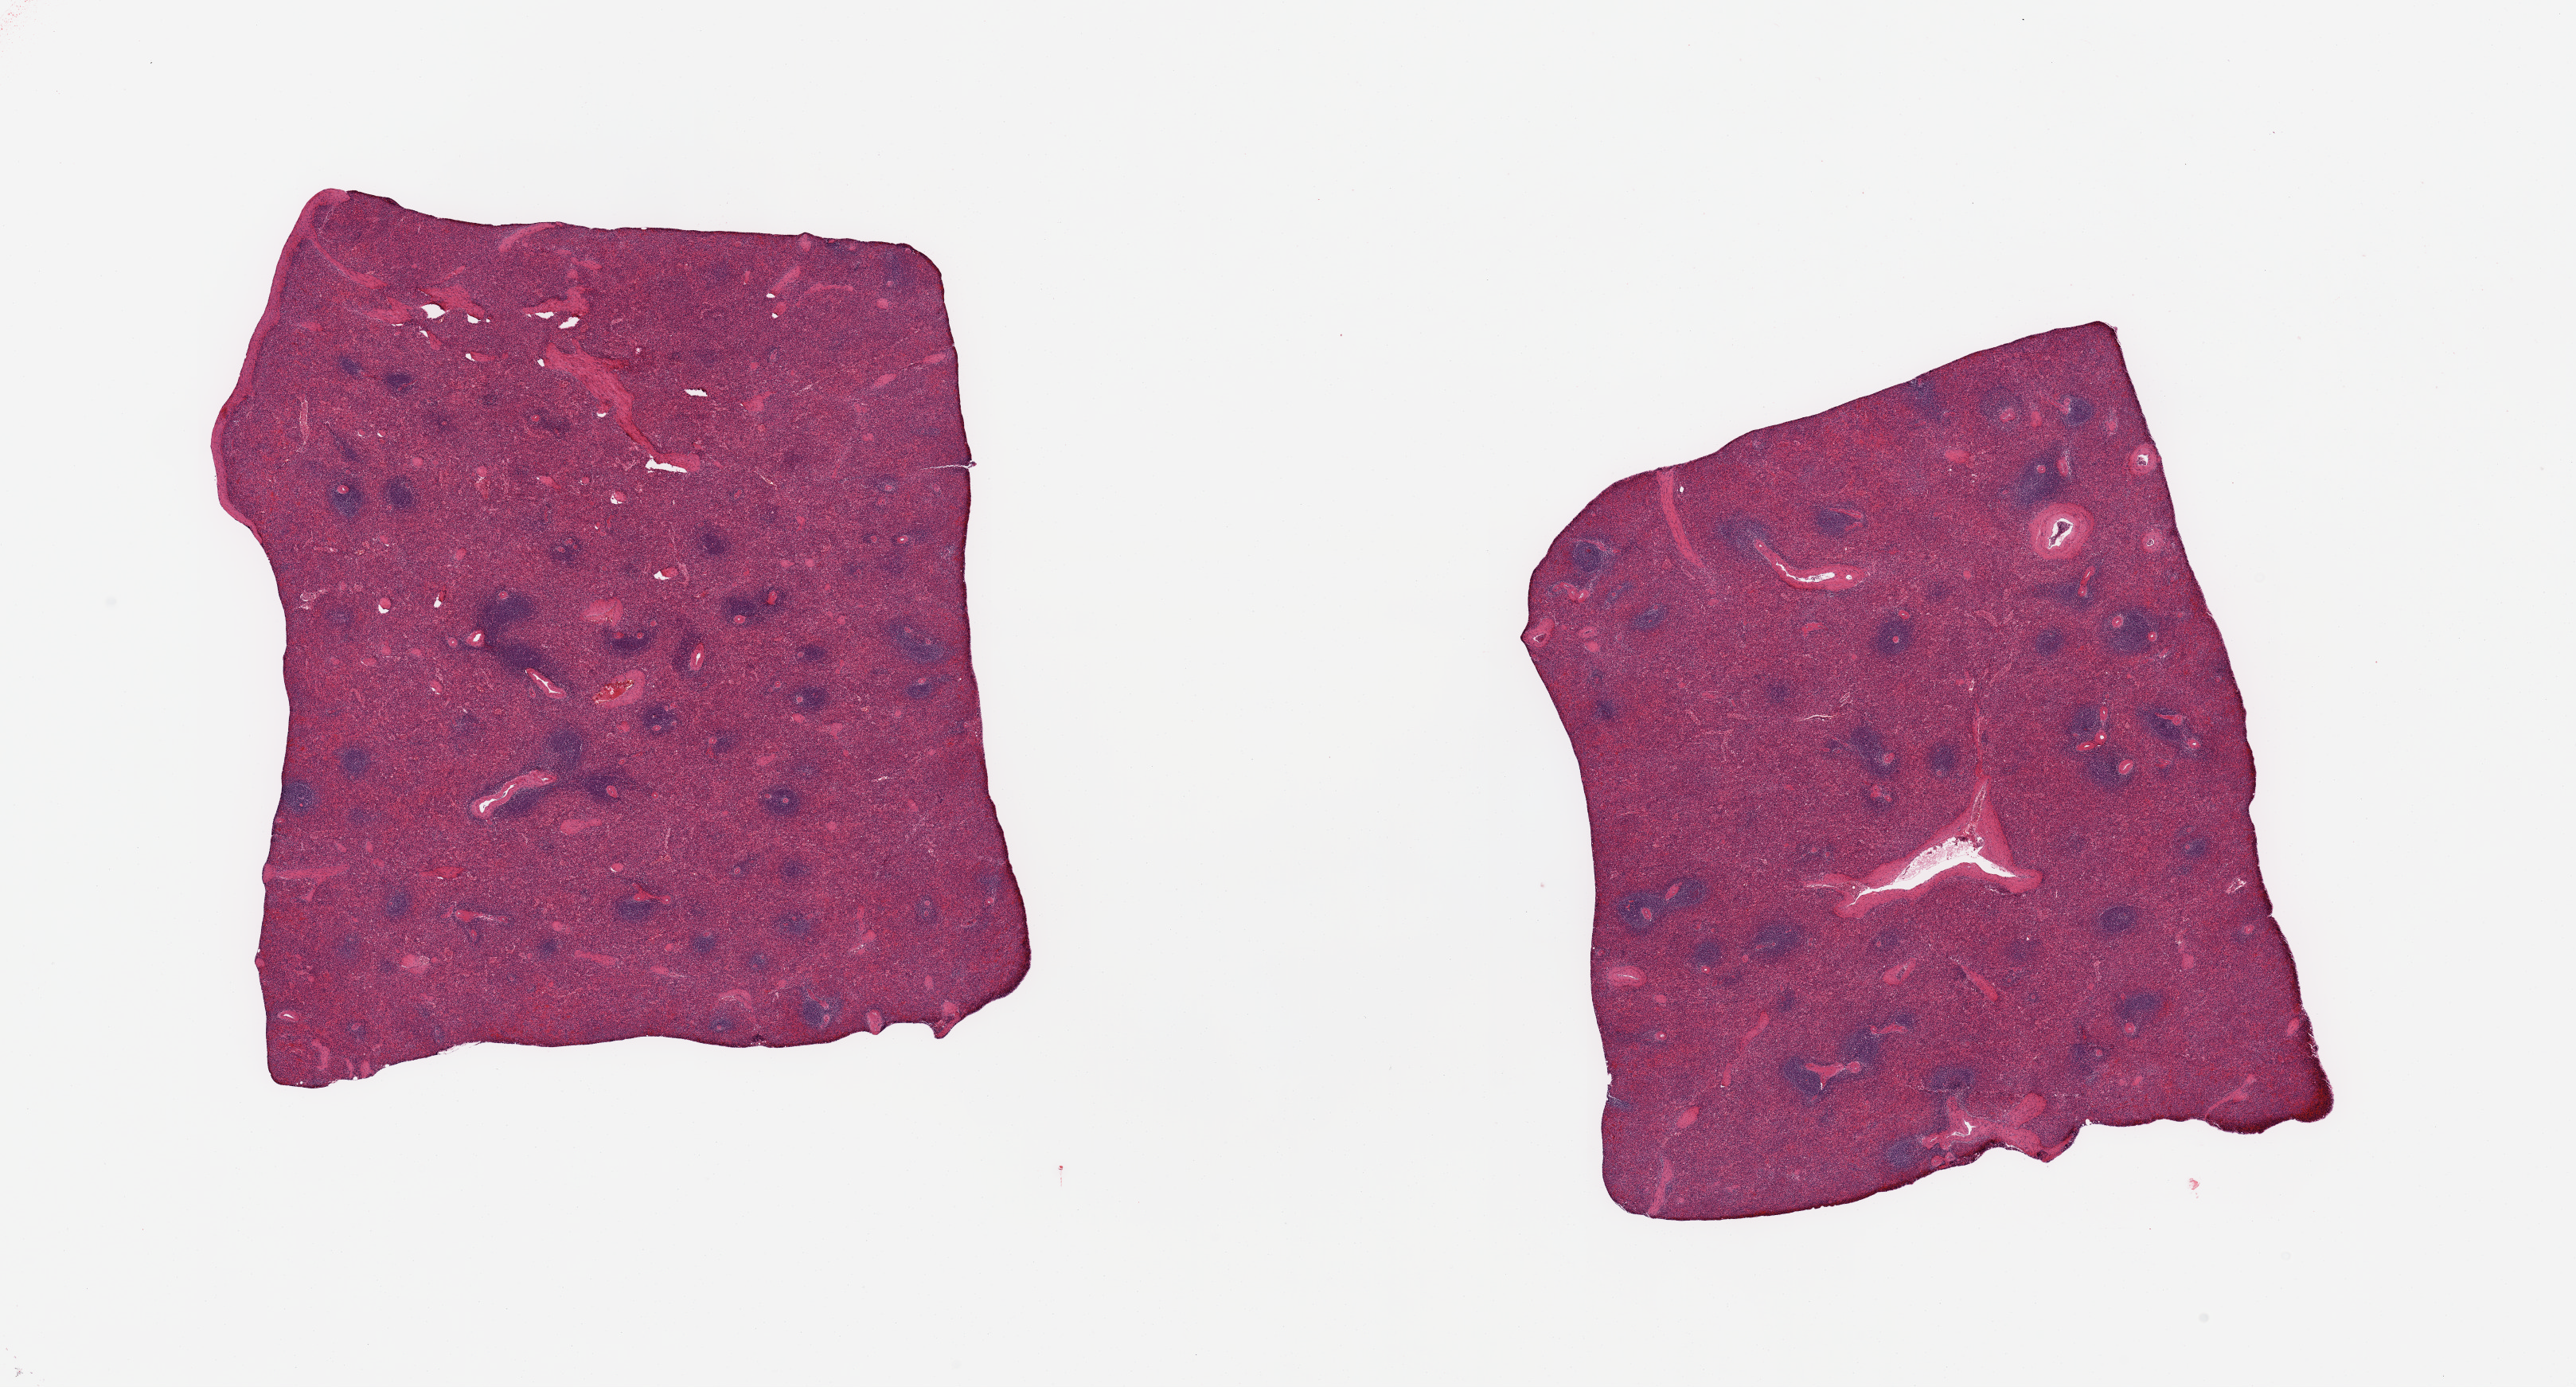
H&E whole-slide image, brightfield — whole scanned area (about 25.6 x 13.8 mm, slide scanned at 20x) shown as a low-resolution overview, PAXgene-fixed, paraffin-embedded tissue, target tissue: spleen, tissue donor sample.
Review note (as recorded): 2 pieces, no abnormalities.